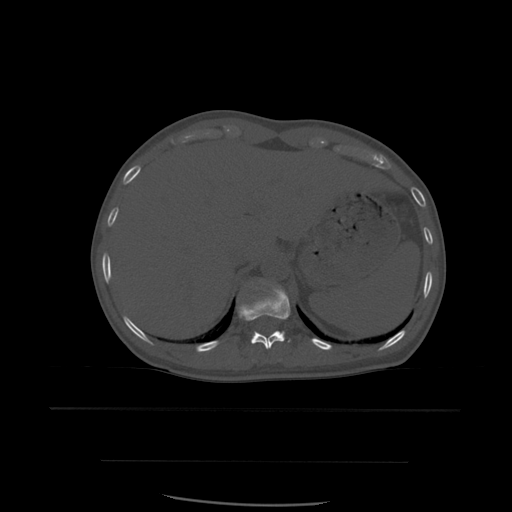
CT including the spine, one axial slice. Position 292 of 574 along the scan axis. Bone window (W 1800 / L 400 HU). 1.25 mm slice thickness. 512 × 512 image matrix. Patient age 48 years. From the clinical record (not read from this slice): primary cancer: lung.
Outlined on this slice (semi-automatically segmented with operator editing):
- T11 vertebra: bounding box (x1, y1, x2, y2) in pixels: (238, 286, 291, 350)